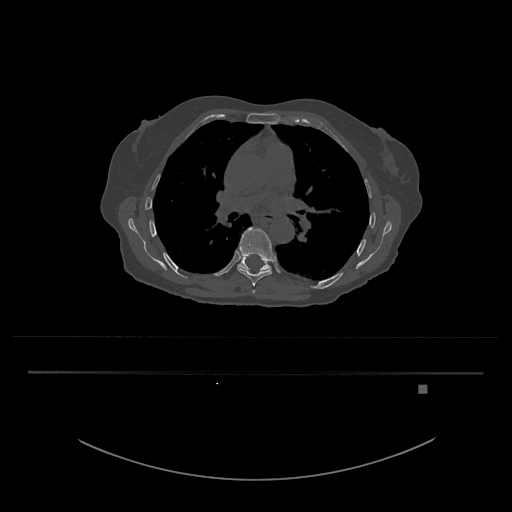
CT including the spine, one axial slice; position 792 of 797 along the scan axis; 120 kVp; bone window (W 1800 / L 400 HU); 0.5 mm slice thickness; 512 × 512 image matrix, field of view 500 × 500 mm. Patient: female, 57 years. Case-level facts recorded for this patient, not image findings: primary cancer: cervical.
Structures marked on this image (semi-automatically segmented with operator editing):
- T8 vertebra: bounding box <237,227,274,286> (left, top, right, bottom; pixels)
- T9 vertebra: <238,257,271,272>